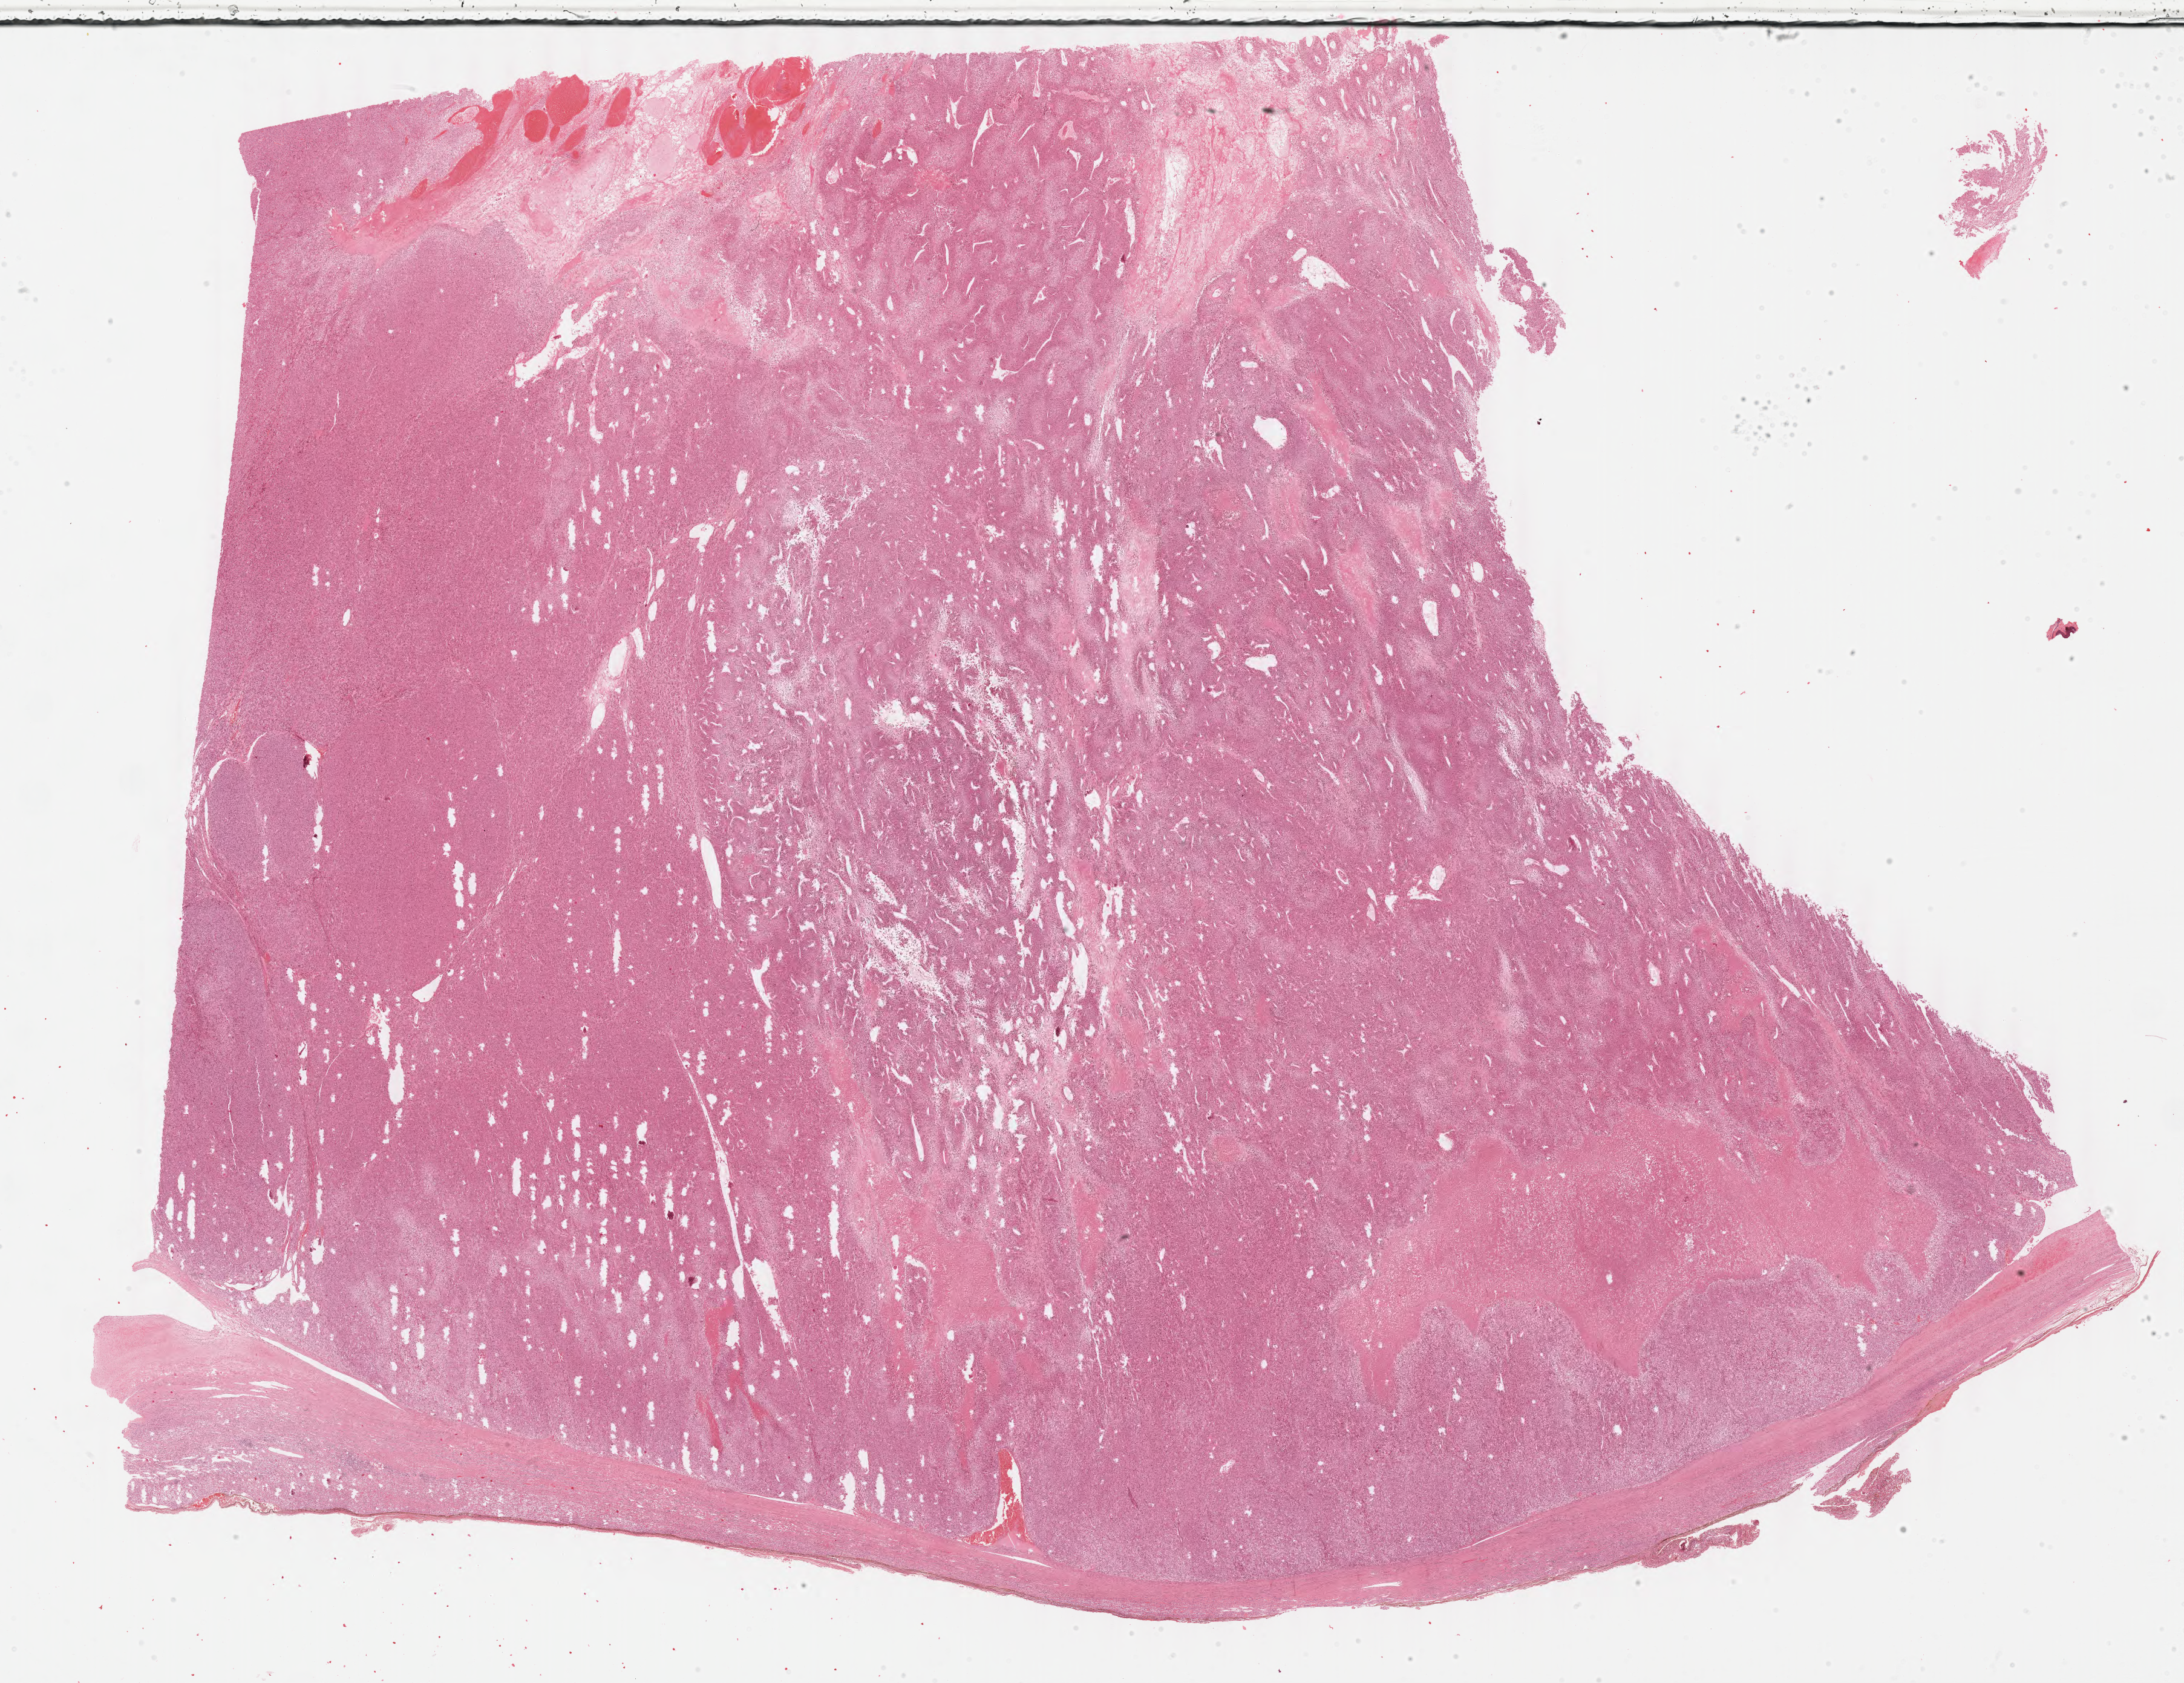
Digitized Hematoxylin and eosin (H&E) stained tissue section (whole slide), shown as a low-resolution overview of the whole scanned area (about 28.5 x 22.0 mm, from a 40x scan). FFPE section. Sample: primary tumour, adrenal cortex. Male, age 42 years at initial diagnosis.
Pathologic diagnosis: Adrenal cortical carcinoma (cortex of adrenal gland).